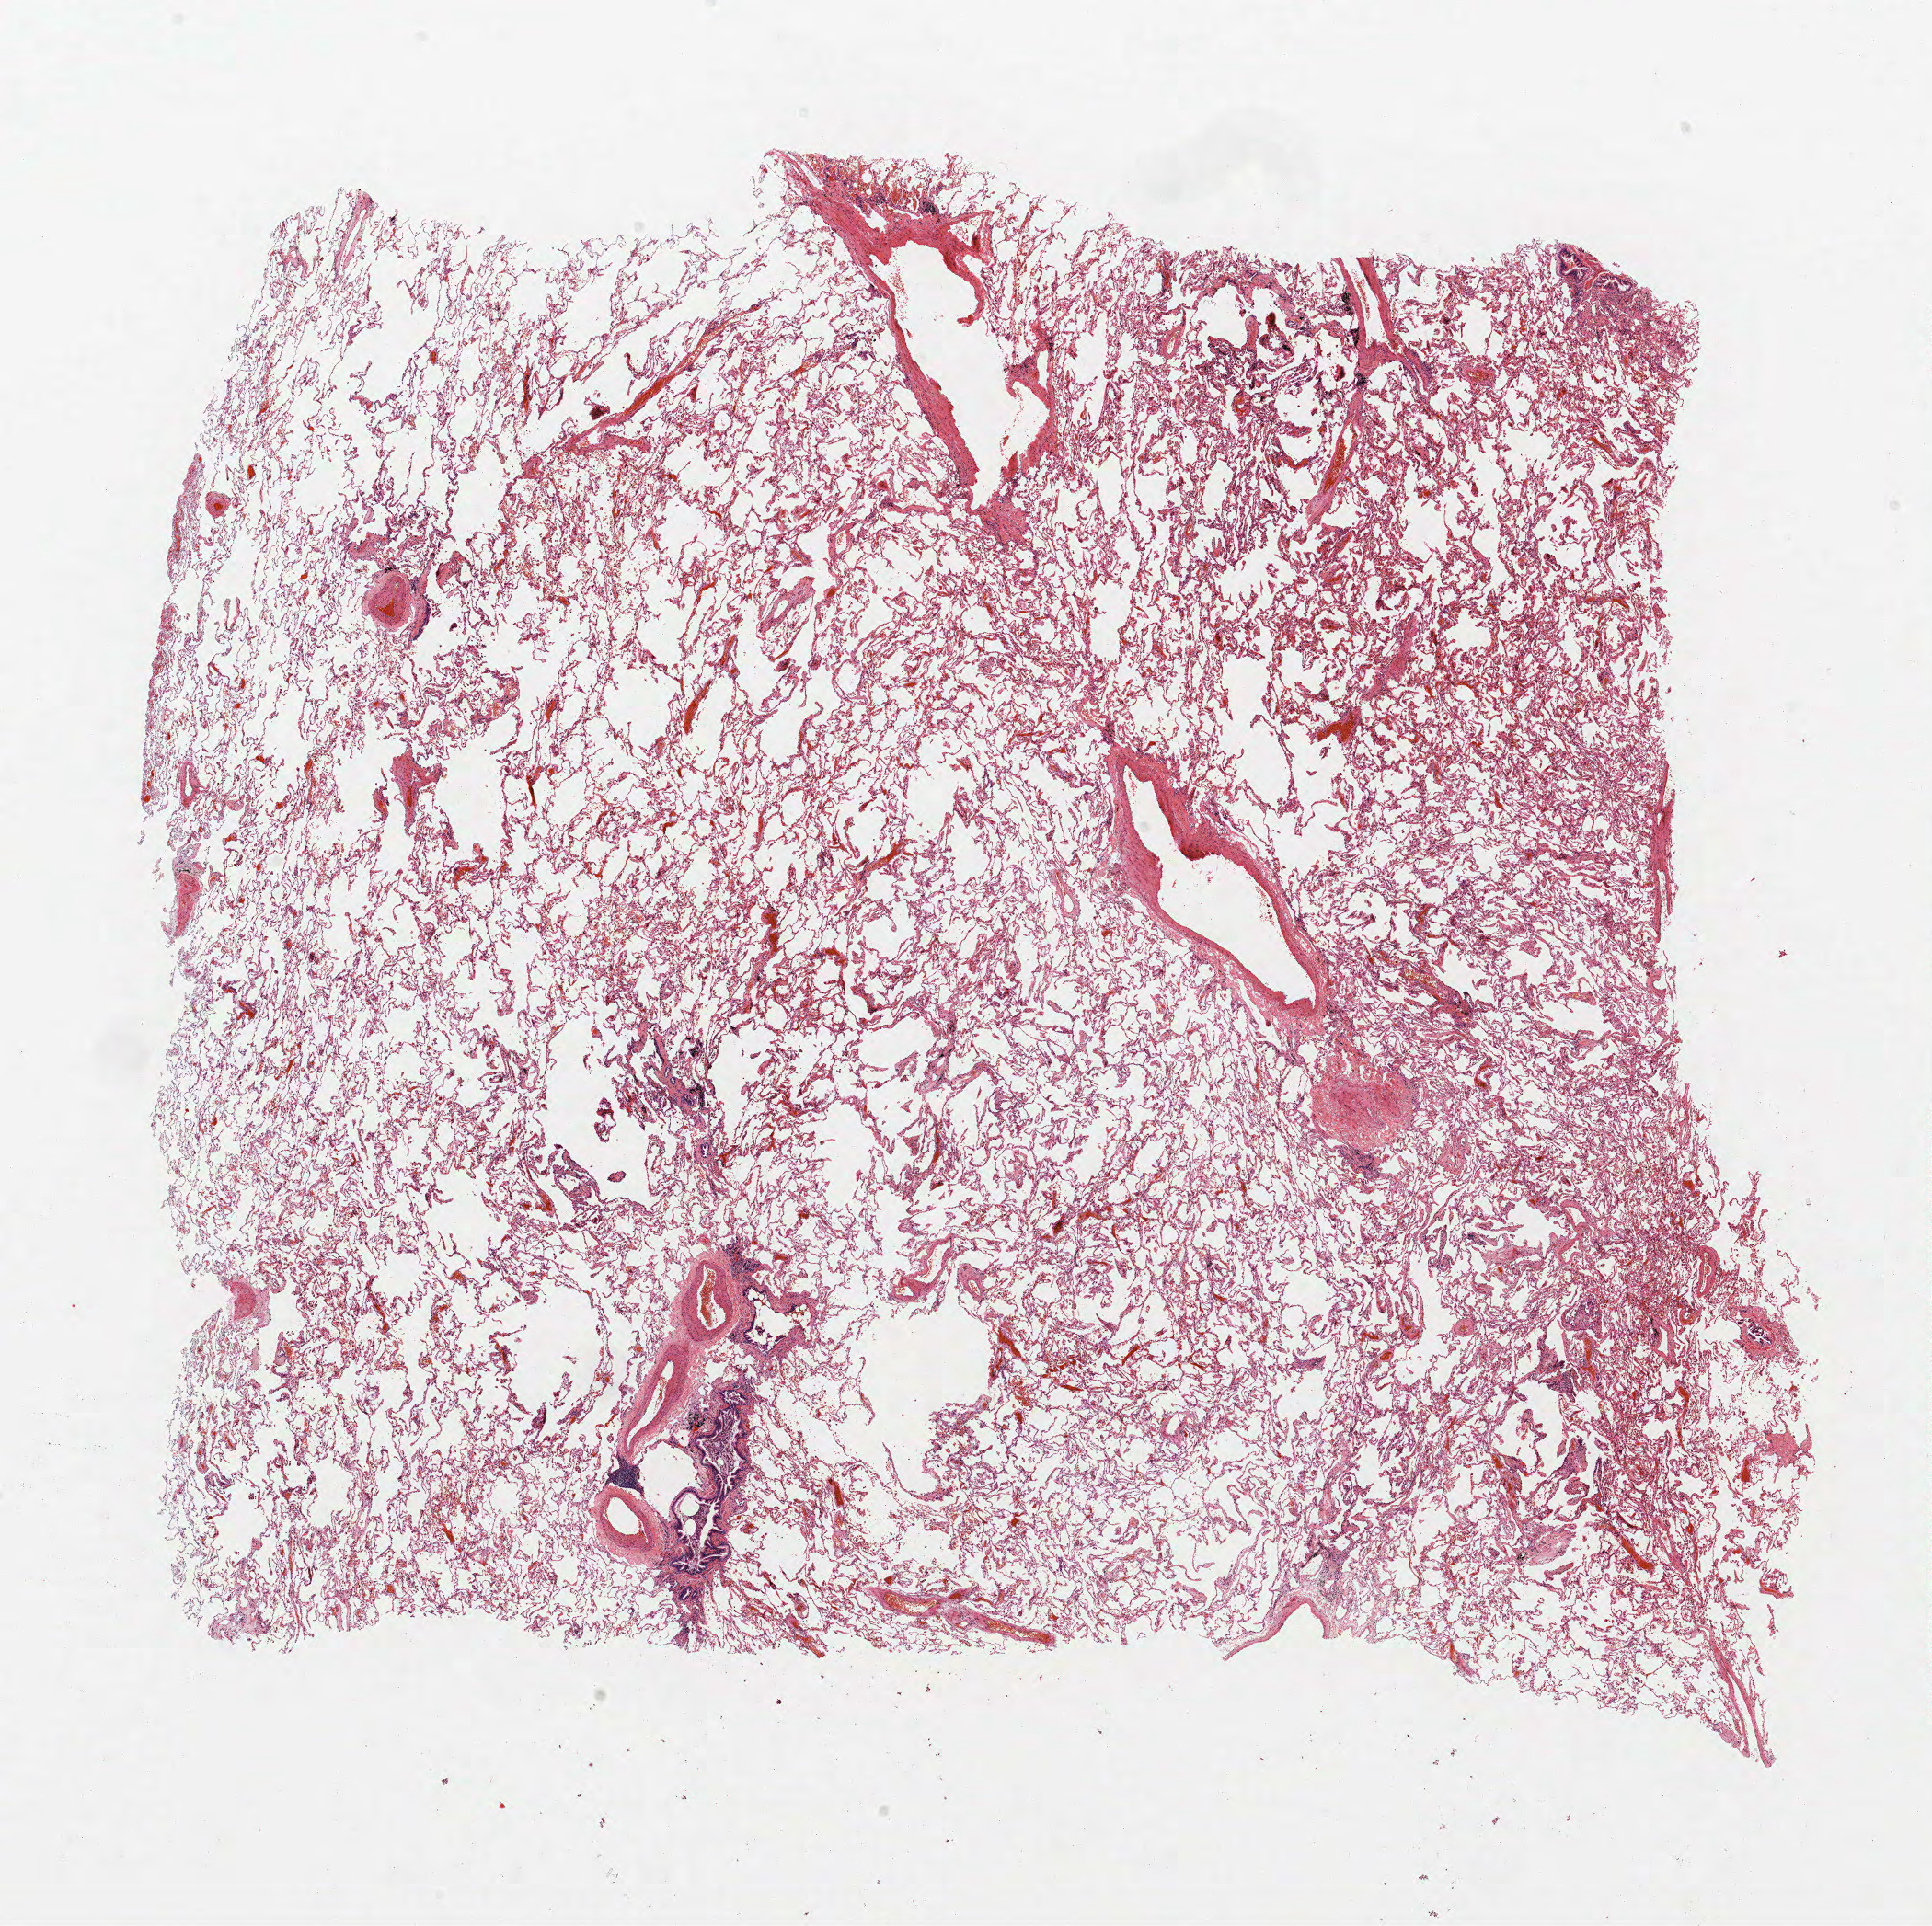
Whole-slide histology image, Hematoxylin and eosin (H&E) stained, low-resolution overview of the scanned area, about 16.8 x 16.8 mm (acquisition: 40x scan). Formalin-fixed paraffin-embedded (FFPE) section. Lung. Male, age 68 at enrolment. Grade: well differentiated (G1).
Stage (AJCC 6th edition): IA. Participant's lung-cancer diagnosis: Bronchiolo-alveolar adenocarcinoma, NOS. Primary tumour location (clinical record): right lower lobe. Tumour size (pathology): 12 mm.